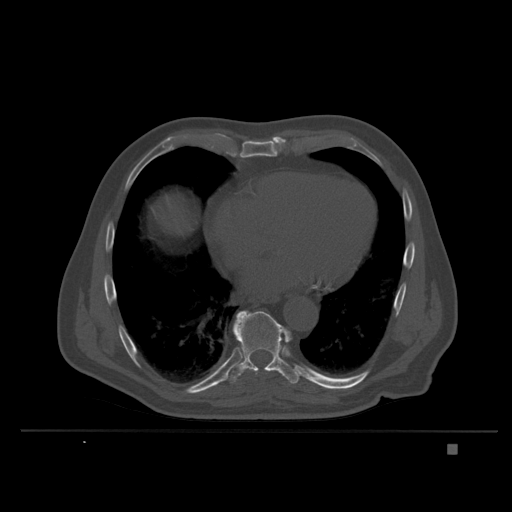
CT including the spine, one axial slice; position 217 of 435 along the scan axis; bone window (W 1800 / L 400 HU); 1.5 mm slice thickness; 512 × 512 image matrix, field of view 434 × 434 mm. Male patient, age 73 years. From the clinical record (not read from this slice): primary cancer: skin.
Structures marked on this image (semi-automatically segmented with operator editing):
- T9 vertebra: bounding box (x1, y1, x2, y2) in pixels: (226, 310, 300, 385)